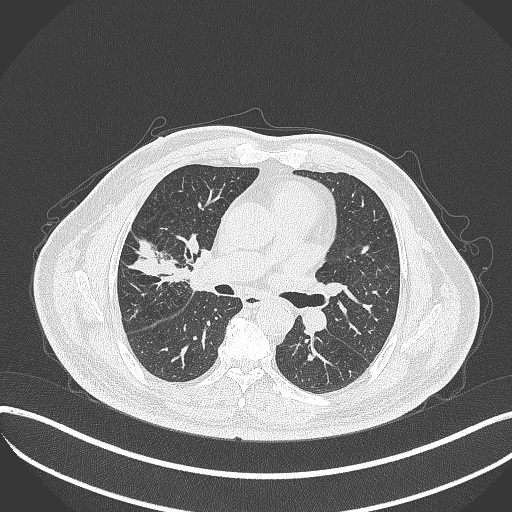
Chest CT, one axial slice; slice 202 of 401 in the series (ordered by position); reconstruction kernel B70f; lung window (W 1500 / L -600 HU); 1 mm slice thickness; 512 × 512 image matrix, field of view 400 × 400 mm. Male patient, age 72 years. From the clinical record (not read from this slice): clinical TNM (as recorded): T1c N0 M0; histopathological grade: G2.
Outlined on this slice (rectangle marked by the reading radiologist):
- lung tumour (recorded histology: squamous cell carcinoma): bounding box <182,228,208,297> (left, top, right, bottom; pixels)